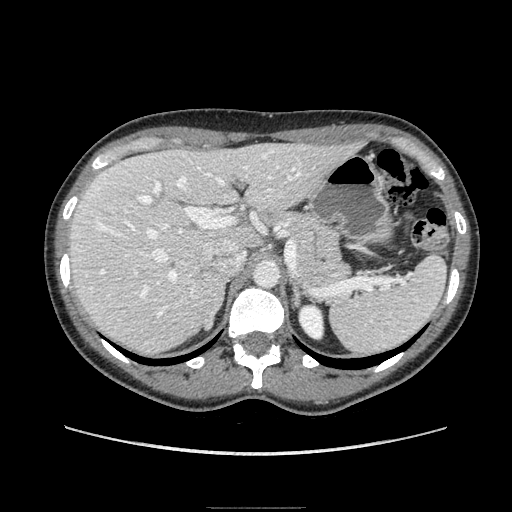
Contrast-enhanced abdominal CT, one axial slice; position 122 of 193 along the scan axis; soft-tissue window (W 400 / L 40 HU); 1.25 mm slice thickness; 512 × 512 image matrix, field of view 380 × 380 mm. Female patient. From the clinical record (not read from this slice): diagnosis: adrenocortical carcinoma; tumour side: right adrenal; tumour size at pathology: 3 cm; Ki-67 index: 4 %; stage (as recorded): 1.
Annotated regions visible in this slice (semi-automatically segmented with operator editing):
- mass: bounding box [x1, y1, x2, y2] px = [193, 272, 224, 328]